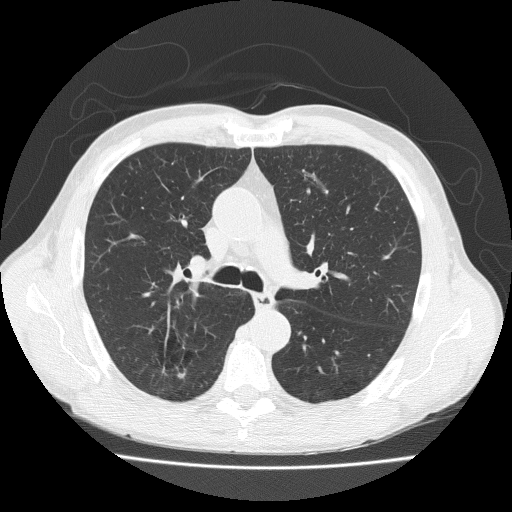
Axial slice from a low-dose chest CT screening exam, baseline screening round, lung window (W 1500 / L -600 HU), 2 mm slice thickness, 120 kVp, slice 73 of 203 in the series. Male, age 73 years at enrolment.
Expert reader's lesion annotation, bounding box <144,333,194,380> (left, top, right, bottom; pixels). No non-calcified nodule or mass ≥4 mm was recorded by the screening reader at this exam. Later outcome: lung cancer diagnosed 777 days after this screen — adenosquamous carcinoma, right upper lobe, well differentiated (G1), stage IA (AJCC 6th edition), 20 mm at pathology.